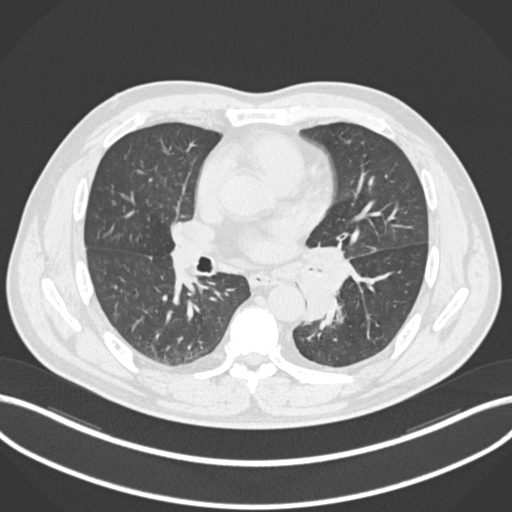
Chest CT, one axial slice. Position 117 of 223 along the scan axis. 120 kVp. Lung window (W 1500 / L -600 HU). 512 × 512 image matrix, field of view 400 × 400 mm. Male patient, age 50 years. Case-level facts recorded for this patient, not image findings: clinical TNM (as recorded): T2a N3 M0.
Outlined on this slice (bounding box drawn by a radiologist):
- lung tumour (recorded histology: squamous cell carcinoma): bounding box <295,244,359,327> (left, top, right, bottom; pixels)